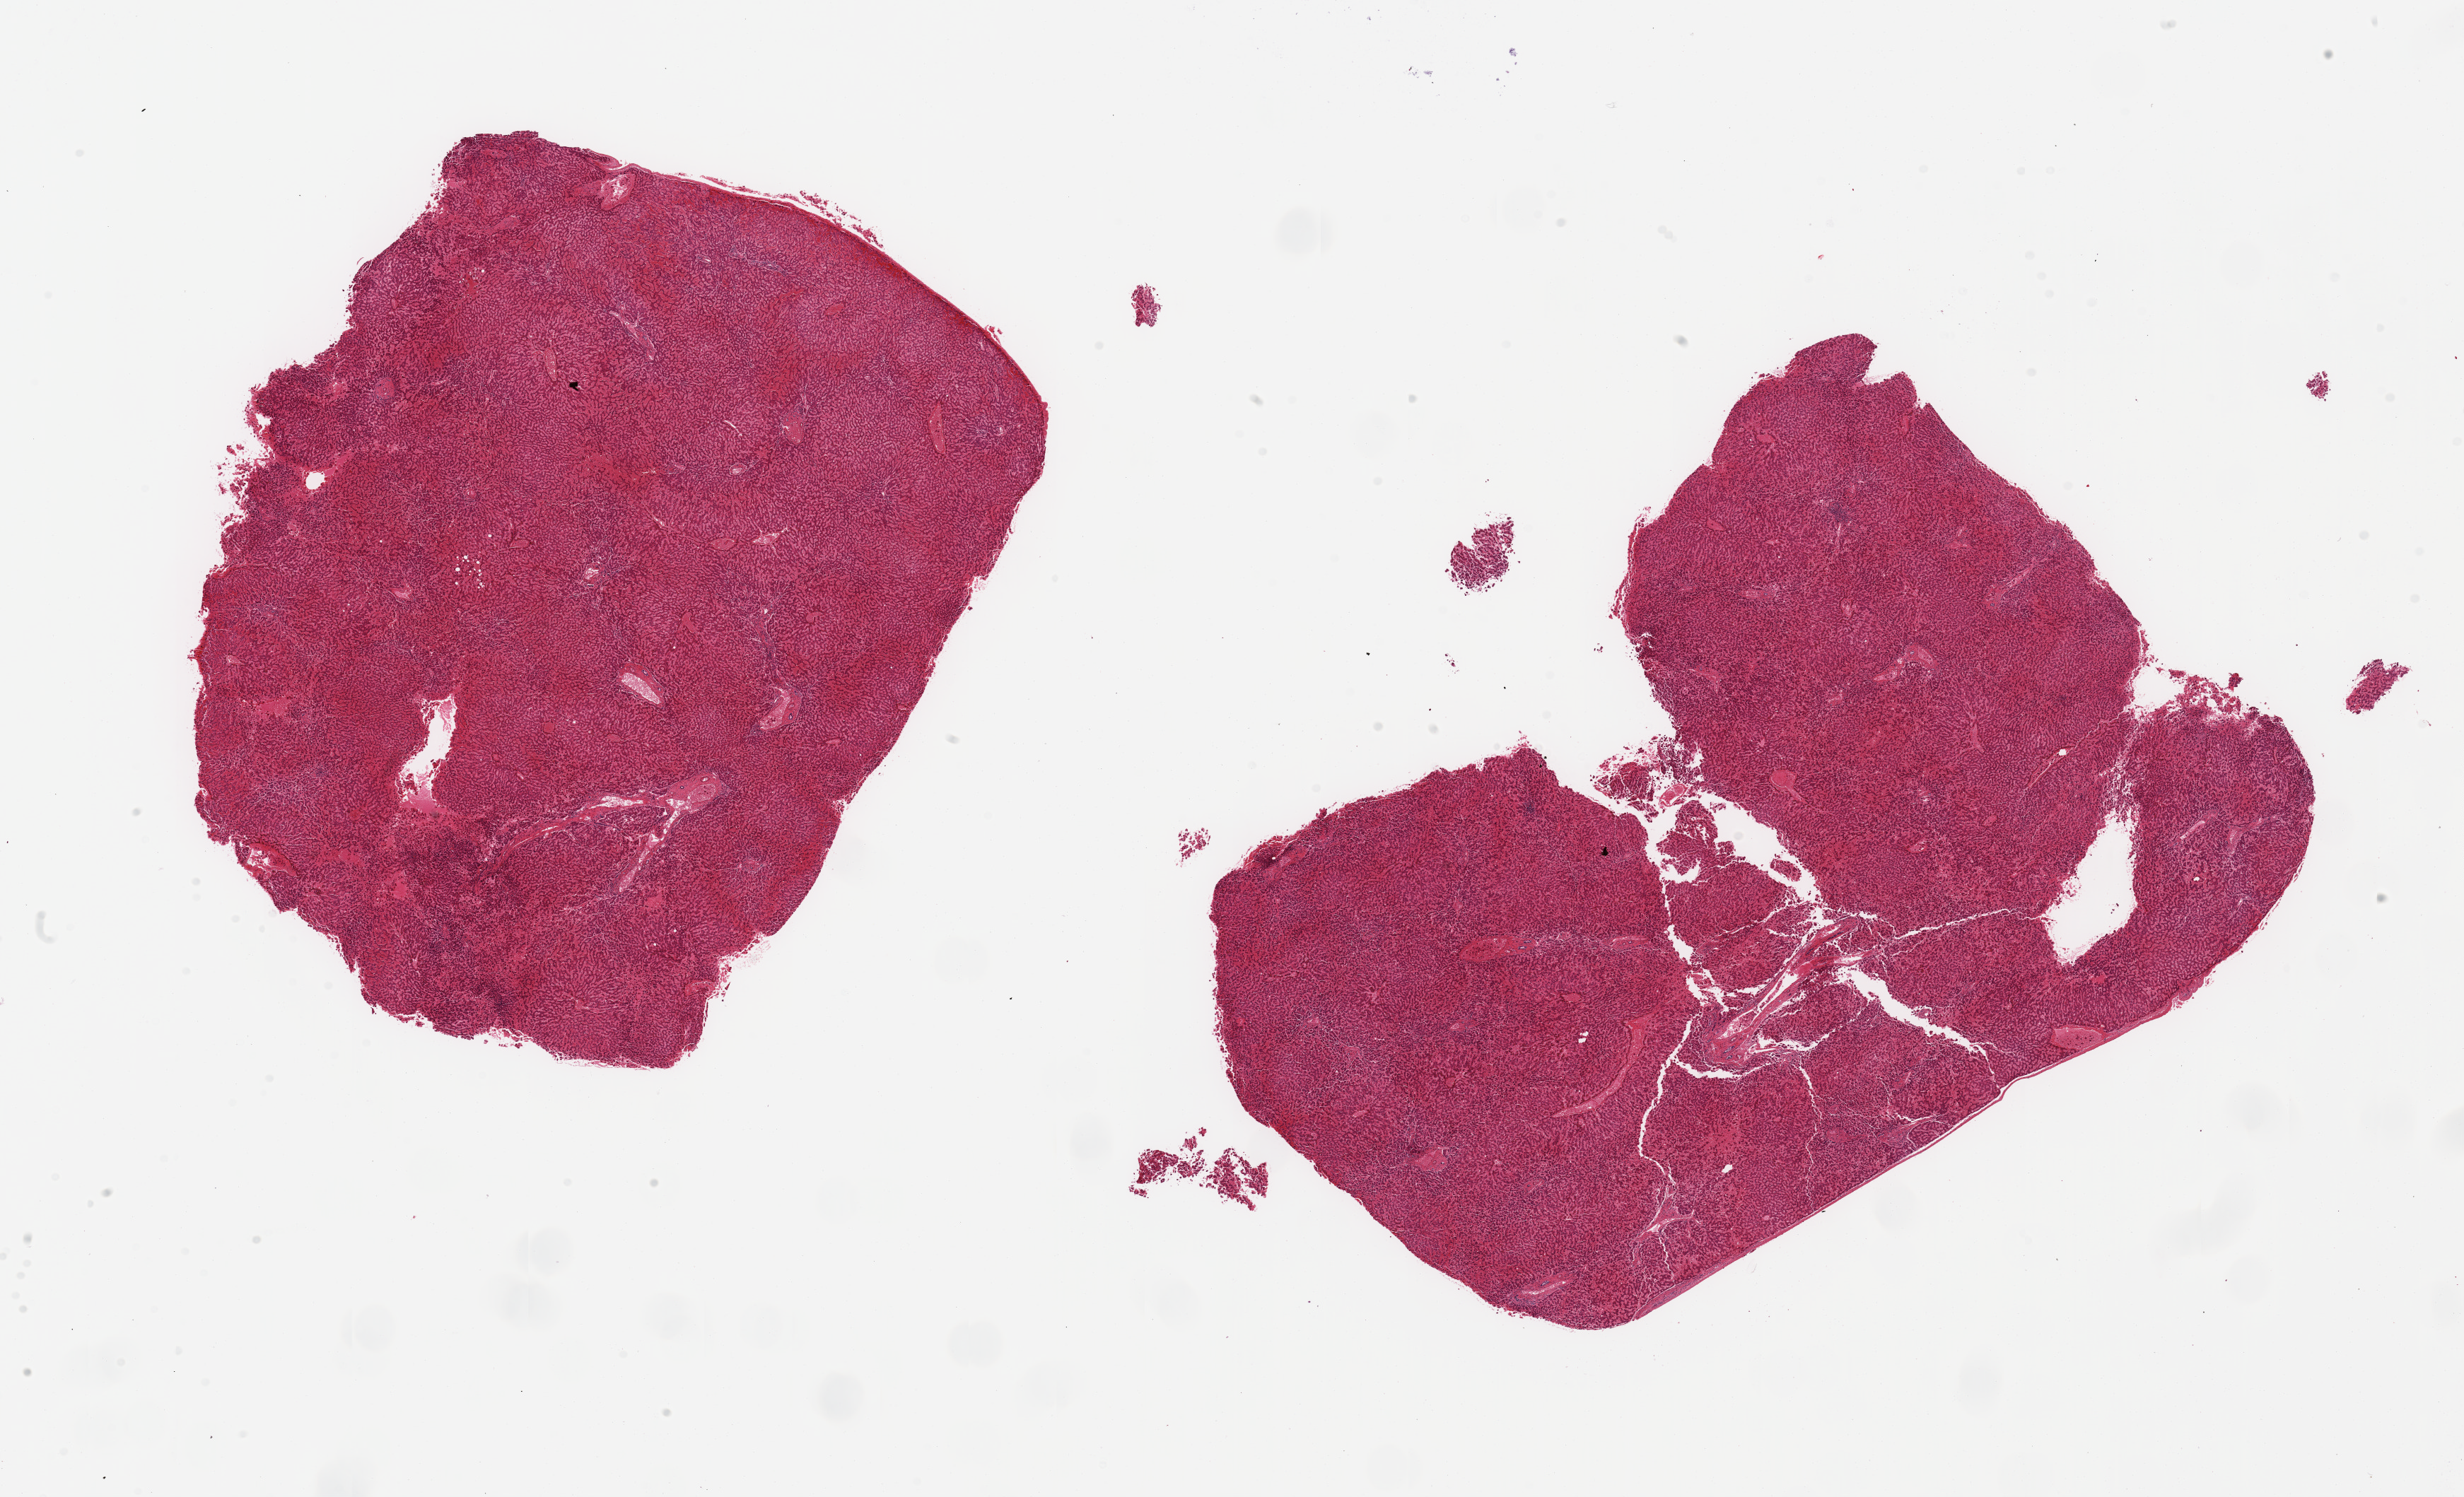
Digitized haematoxylin and eosin-stained section, brightfield — a low-resolution overview of the entire scanned area, about 27.6 x 16.8 mm (acquisition: 20x scan); PAXgene-fixed, paraffin-embedded tissue; sampled site (target tissue): liver; tissue donor sample. Donor sex: female.
• reviewer comment on this tissue sample: 2 pieces, moderate-marked passive congestion